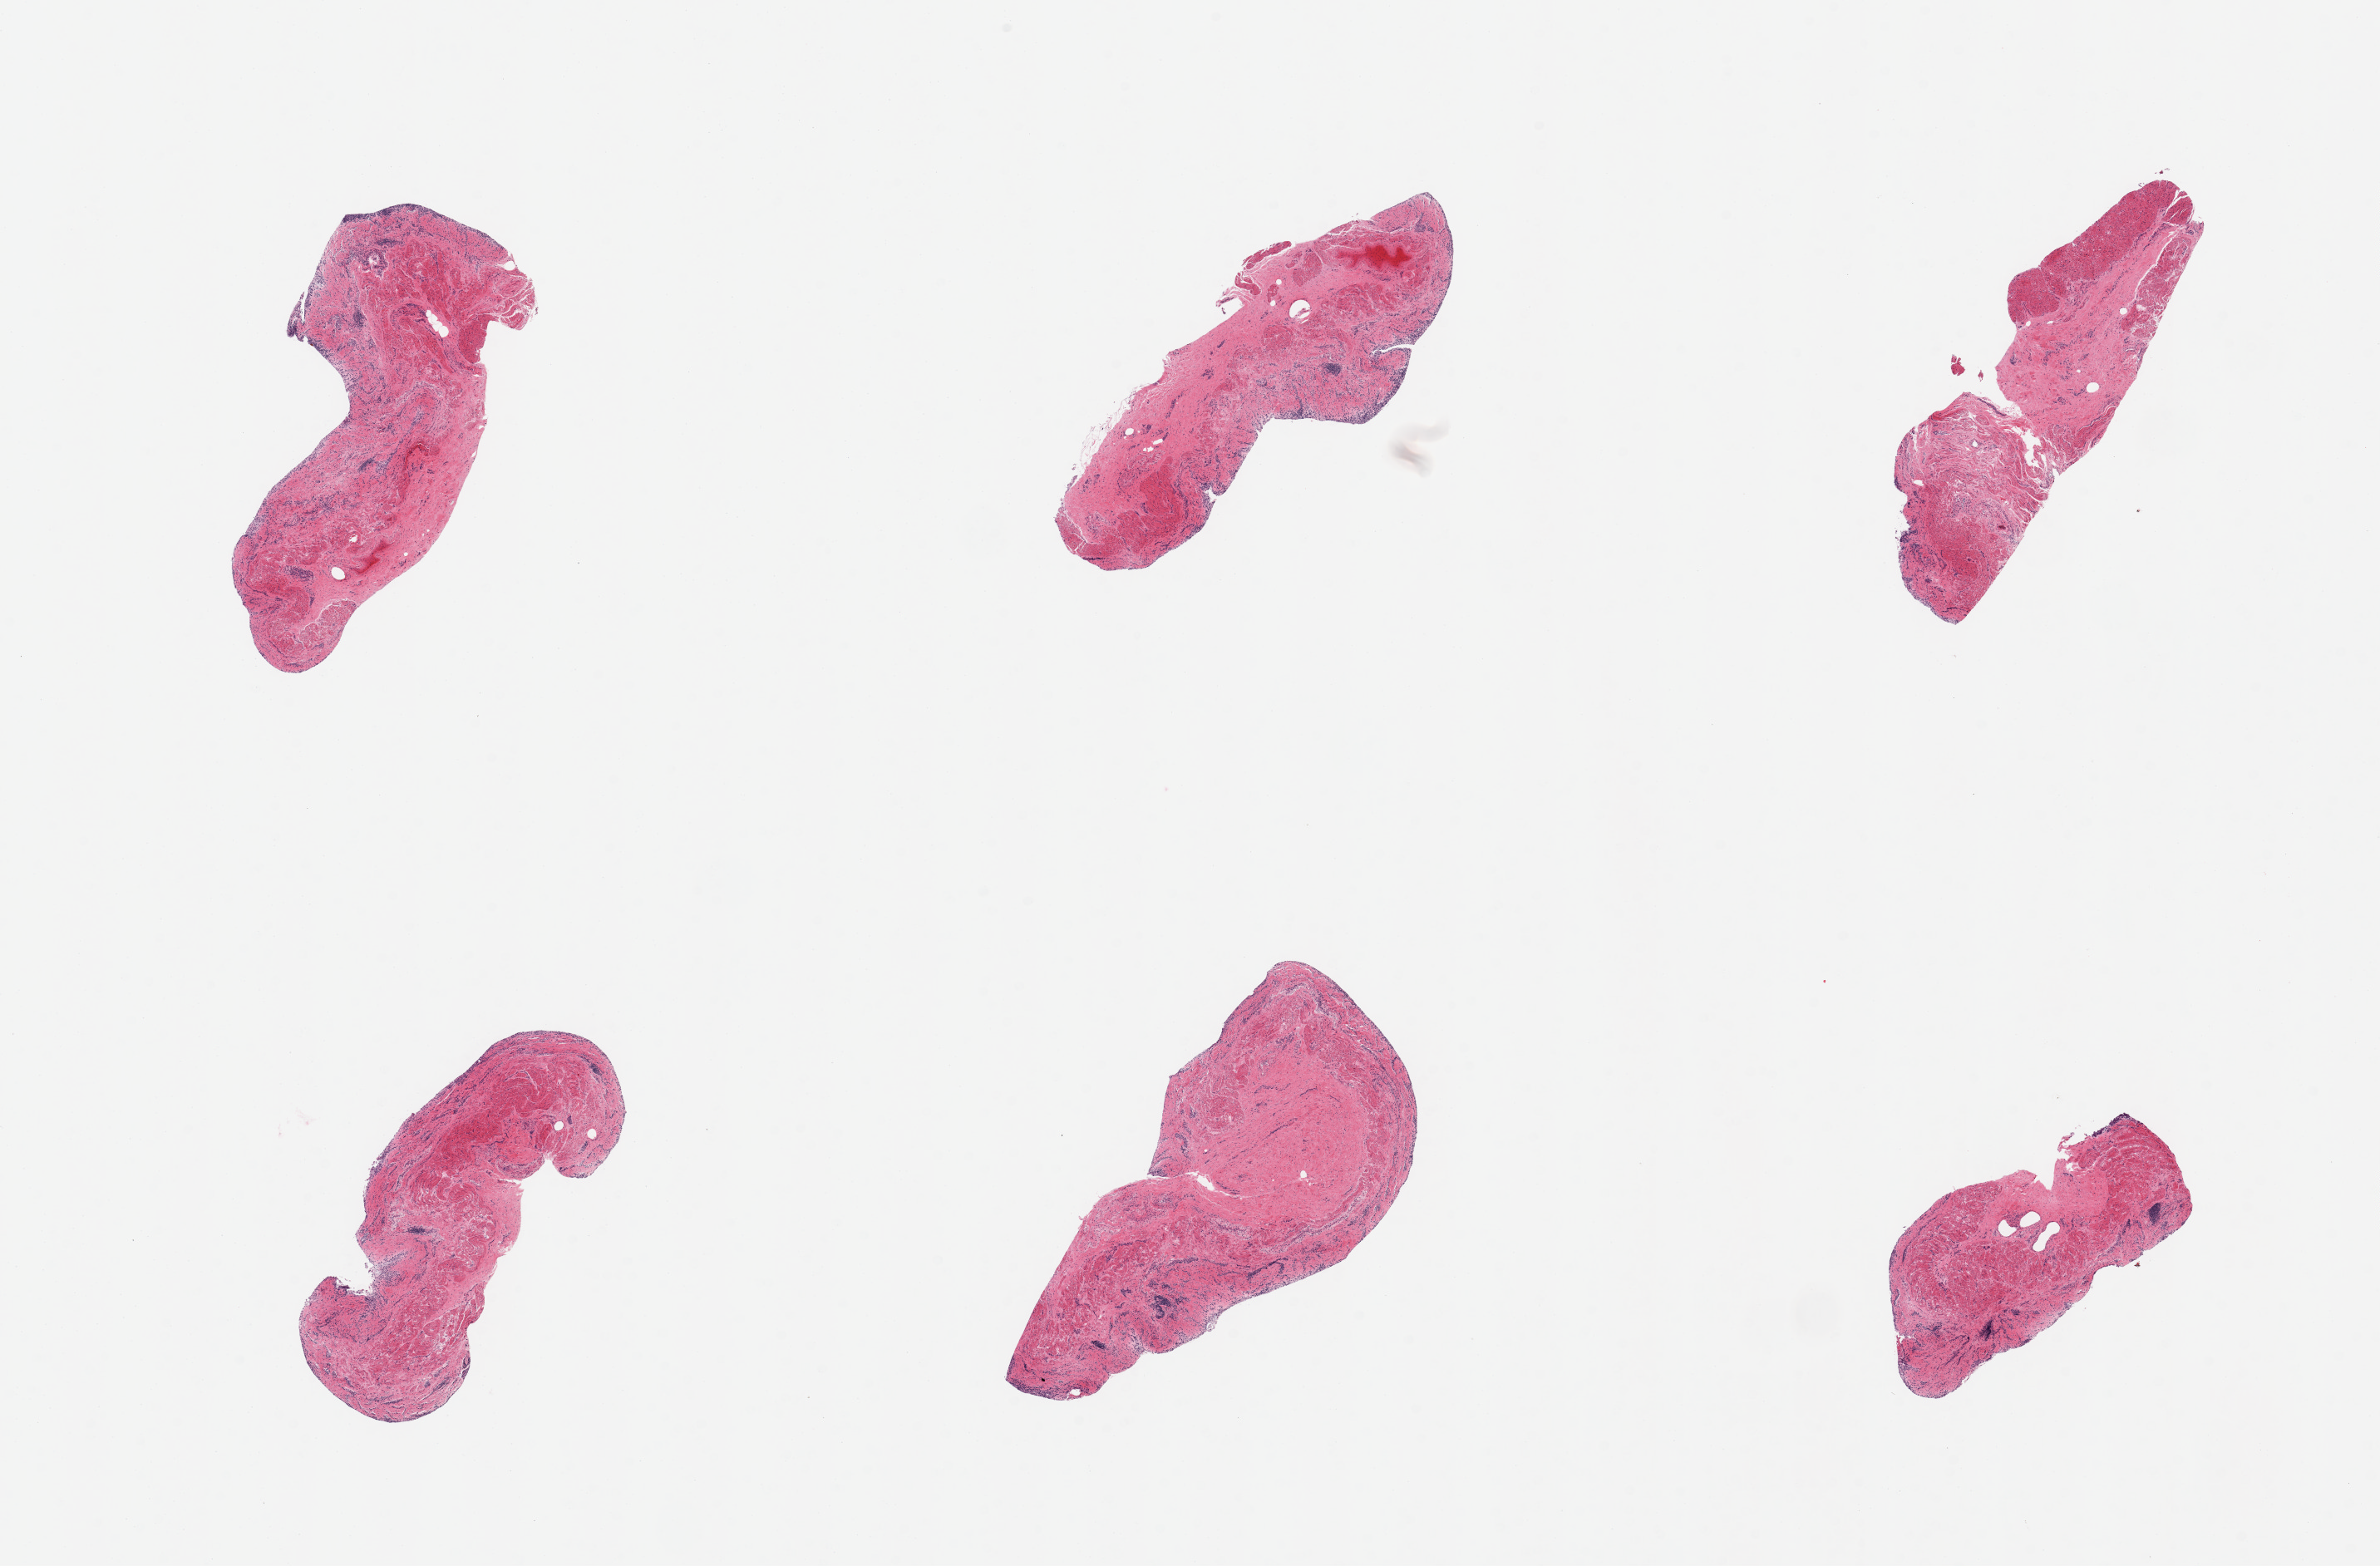
Whole-slide image, H&E stain, brightfield, shown as a low-resolution overview of the whole scanned area (about 22.6 x 14.9 mm); PAXgene-fixed paraffin-embedded (PFPE) section; section of esophageal mucous membrane (target tissue); tissue donor sample. Donor: male.
Reviewer comment on this tissue sample: 6 pieces; mucosa denuded.